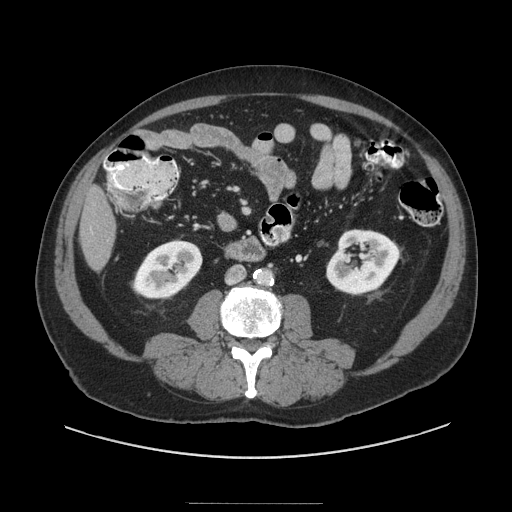
Contrast-enhanced abdominal CT (liver protocol), one axial slice; position 19 of 91 along the scan axis; 140 kVp; soft-tissue window (W 400 / L 40 HU); 2.5 mm slice thickness; 512 × 512 image matrix. From the clinical record (not read from this slice): diagnosis: hepatocellular carcinoma (patient treated with transarterial chemoembolisation; whether this scan precedes or follows treatment is not stated here); TNM stage (as recorded): Stage-I.
Outlined on this slice (semi-automatic segmentation, software-assisted and operator-edited):
- liver parenchyma outside the tumour (the mass and vessels are separate outlines, so this box may not span the whole liver): box from (x=80, y=186) to (x=116, y=270) px